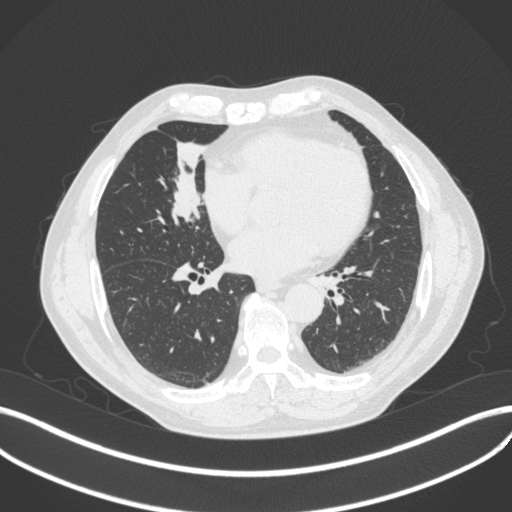
Chest CT, one axial slice; lung window (W 1500 / L -600 HU); 1 mm slice thickness; 512 × 512 image matrix, field of view 400 × 400 mm. Male patient, age 61 years. From the clinical record (not read from this slice): clinical TNM (as recorded): T2b N1 M0.
Structures marked on this image (bounding box drawn by a radiologist):
- lung tumour (recorded histology: squamous cell carcinoma): box from (x=170, y=161) to (x=210, y=232) px